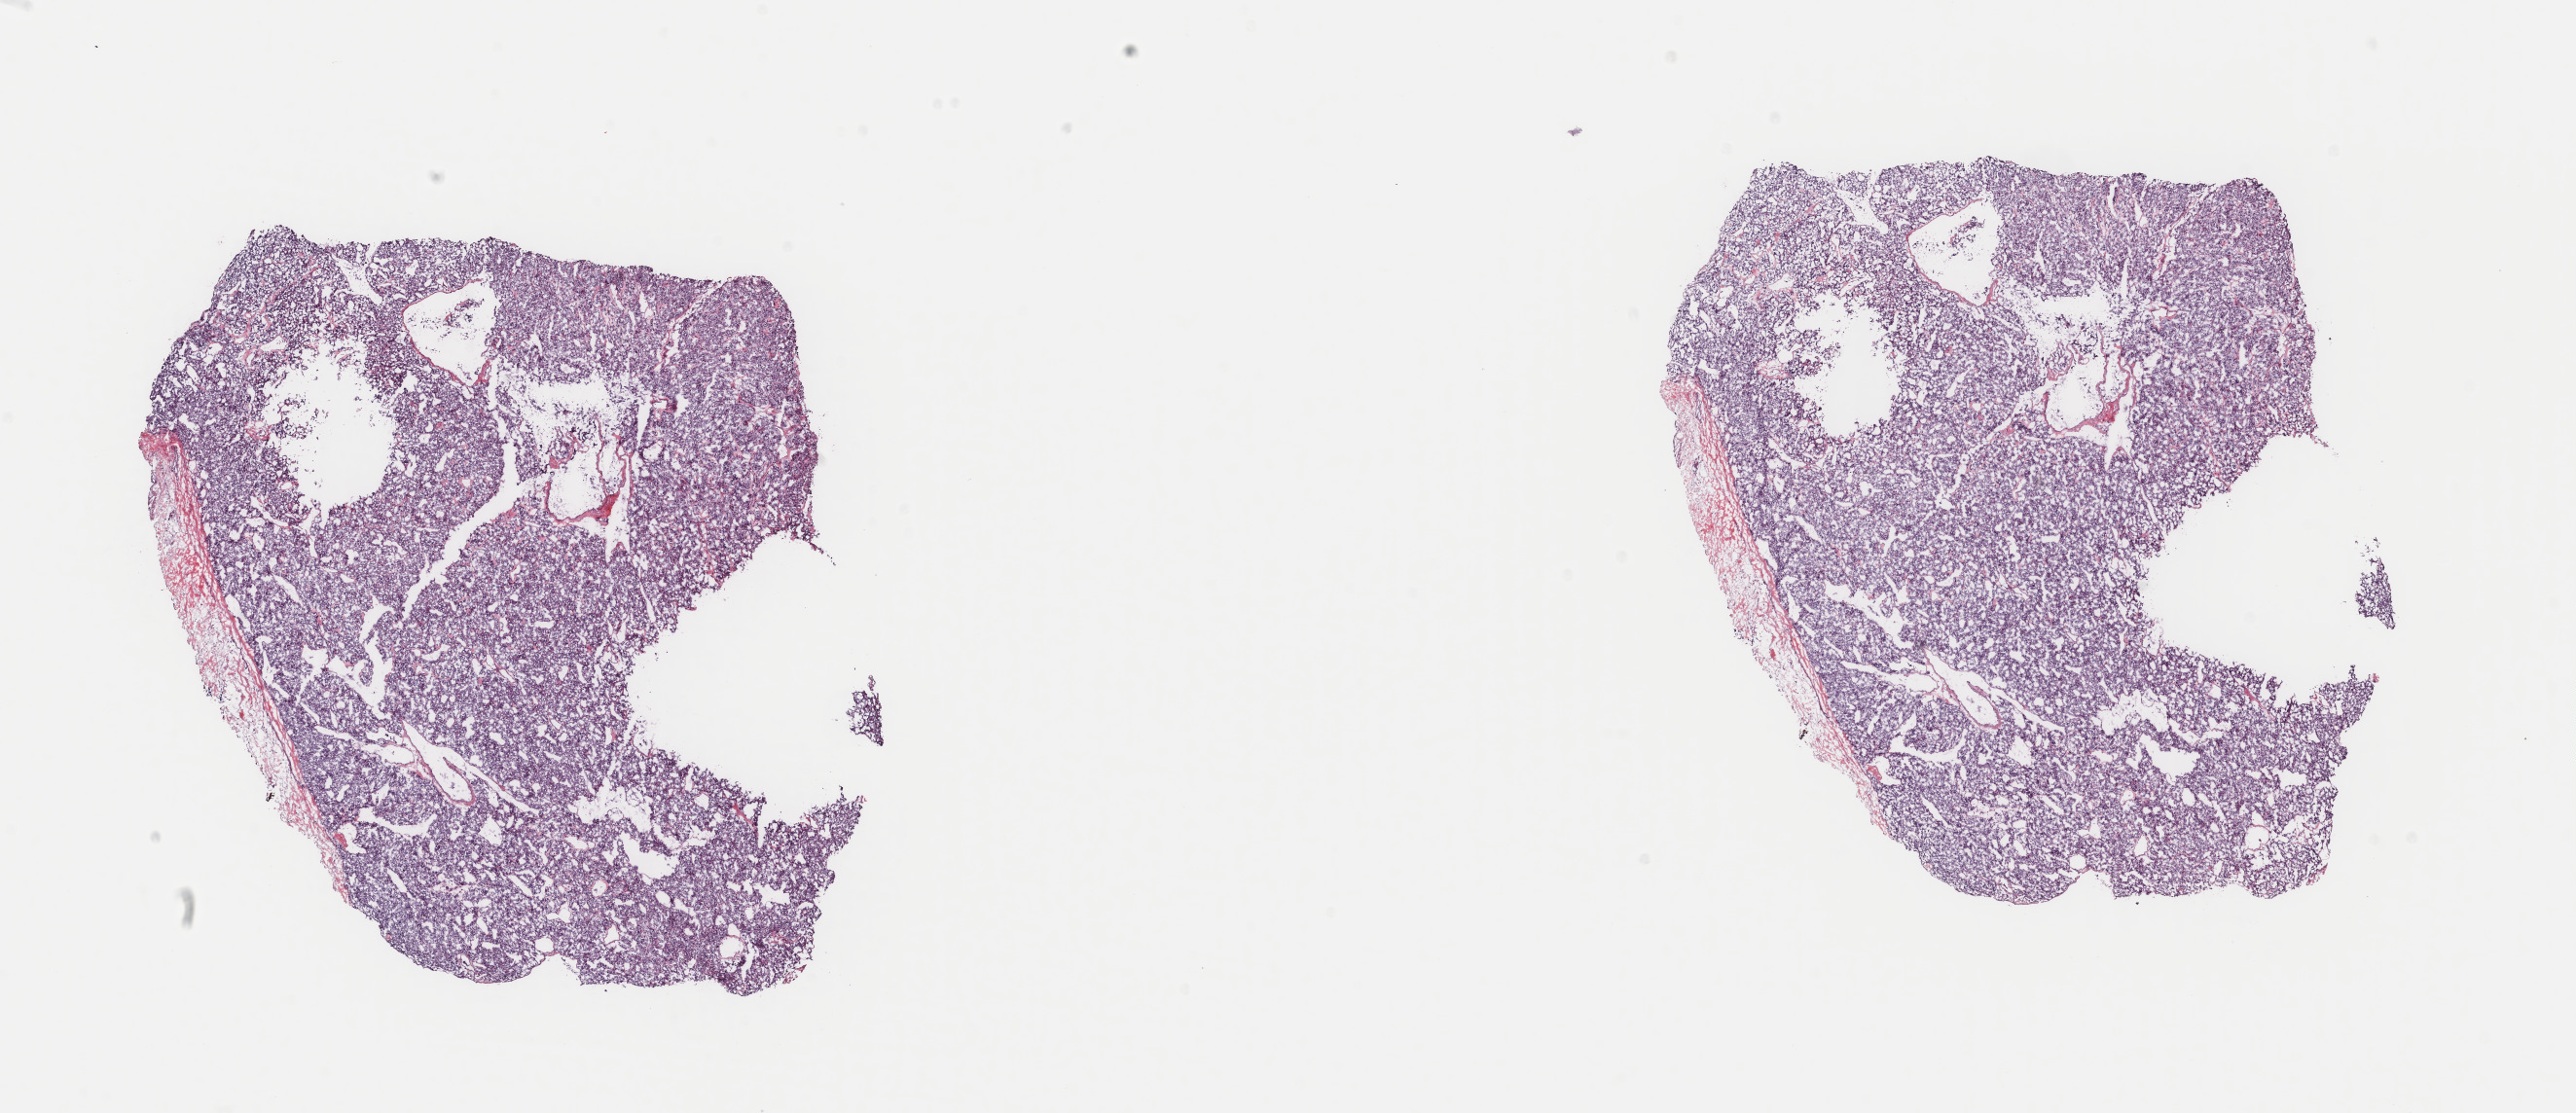
Whole-slide histology image, H&E-stained, a low-resolution overview of the entire scanned area, about 21.0 x 9.1 mm, frozen section from the top of the tissue portion, primary tumour sample. Male patient; age at initial diagnosis 41 years. Pathologist review of this section (percent, as recorded): tumour cells 100%, tumour nuclei 95%, normal cells 0%, stromal cells 0%, necrosis 0%. Infiltration values recorded for this section: lymphocyte infiltration 0%, monocyte infiltration 0%, neutrophil infiltration 0%.
* pathologic diagnosis: Extra-adrenal paraganglioma, NOS (thorax, NOS)